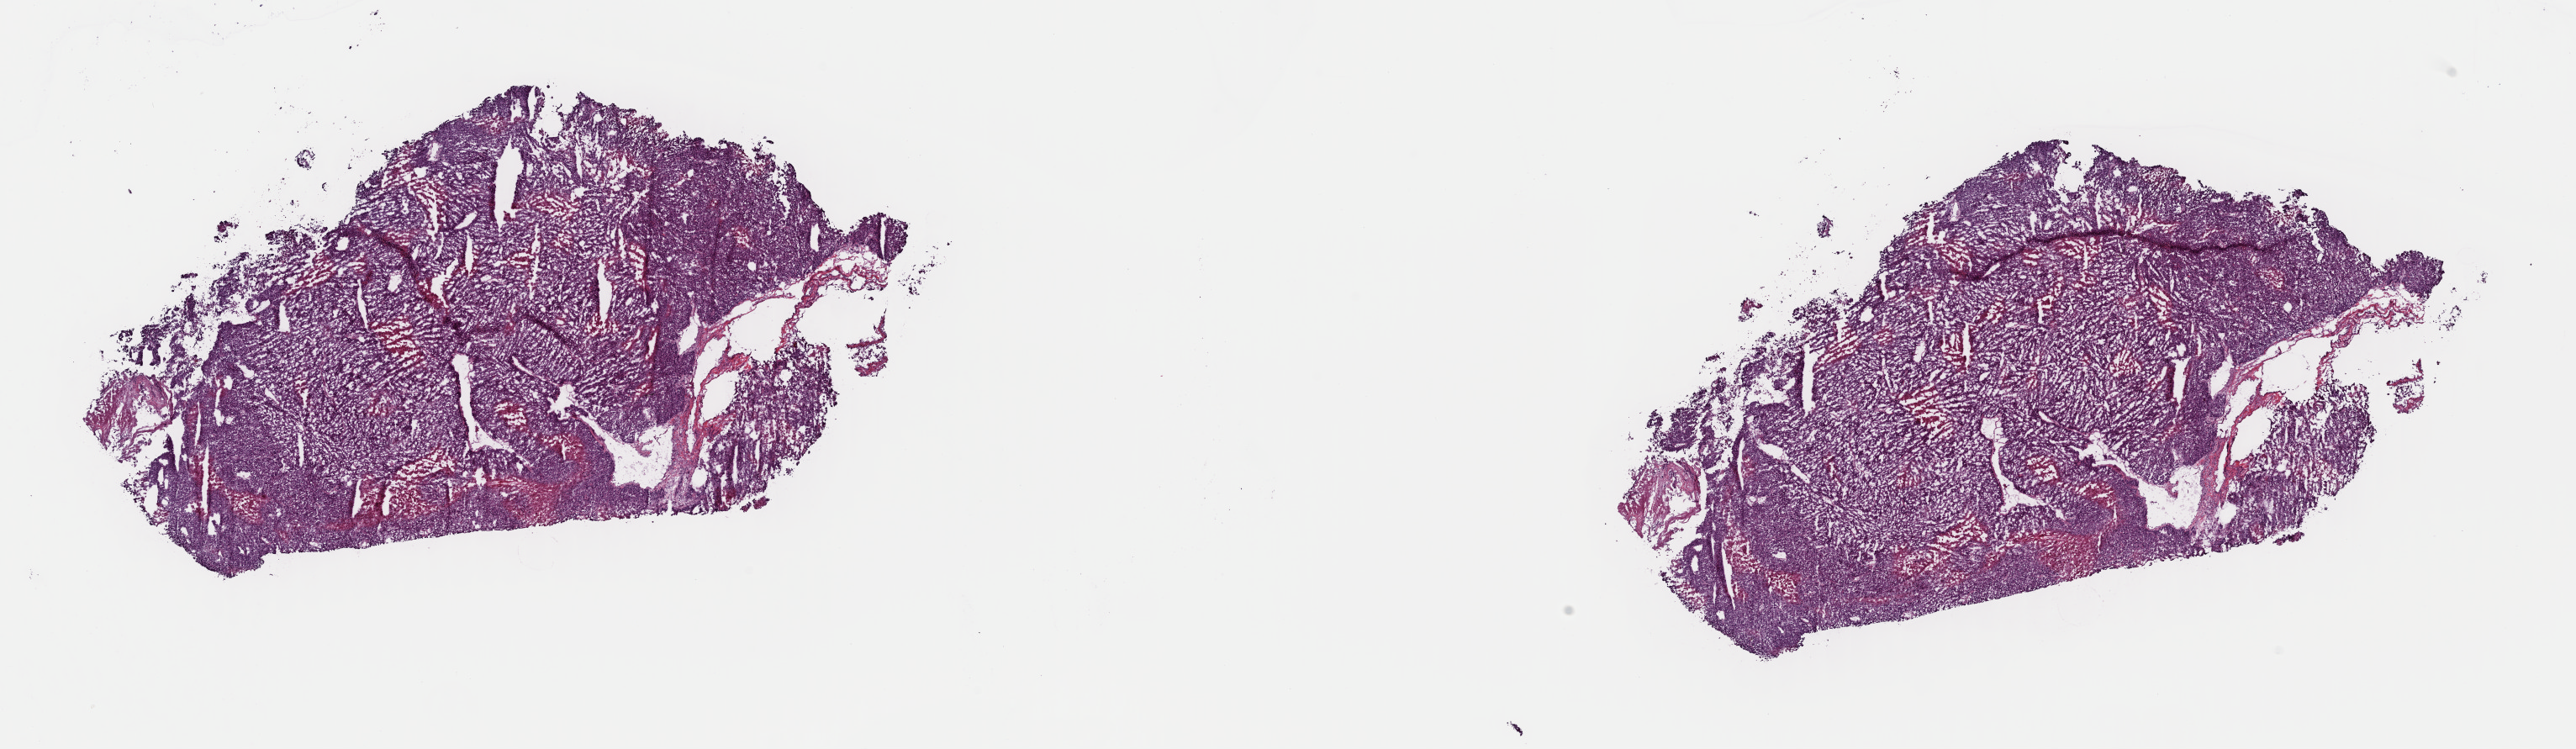
H&E-stained whole-slide image — a low-resolution overview of the entire scanned area, about 24.2 x 7.0 mm, frozen section from the top of the tissue portion, sample: primary tumour, adrenal cortex. Patient: female, age at initial diagnosis 25 years. Pathologist review of this section (percent, as recorded): tumour cells 83%, tumour nuclei 95%, normal cells 0%, stromal cells 0%, necrosis 17%. Infiltration values recorded for this section: lymphocyte infiltration 0%, monocyte infiltration 0%, neutrophil infiltration 0%.
- laterality: left
- diagnosis: Adrenal cortical carcinoma (cortex of adrenal gland)